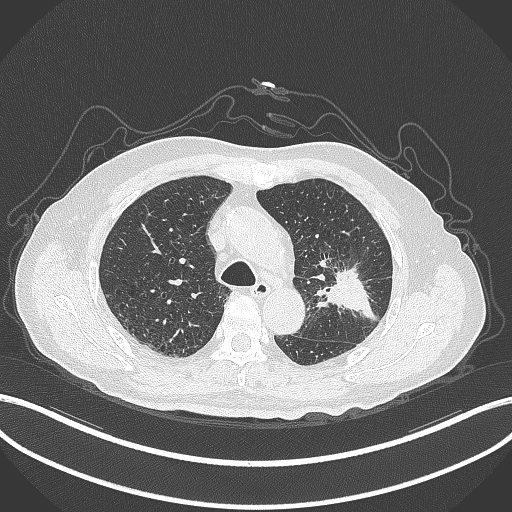
Chest CT, one axial slice; position 203 of 331 along the scan axis; reconstruction kernel B70f; lung window (W 1500 / L -600 HU); 512 × 512 image matrix, field of view 400 × 400 mm. Patient: male, 79 years. From the clinical record (not read from this slice): clinical TNM (as recorded): T2a N1 M1.
Structures marked on this image (rectangle marked by the reading radiologist):
- lung tumour (recorded histology: adenocarcinoma): box from (x=314, y=261) to (x=380, y=321) px